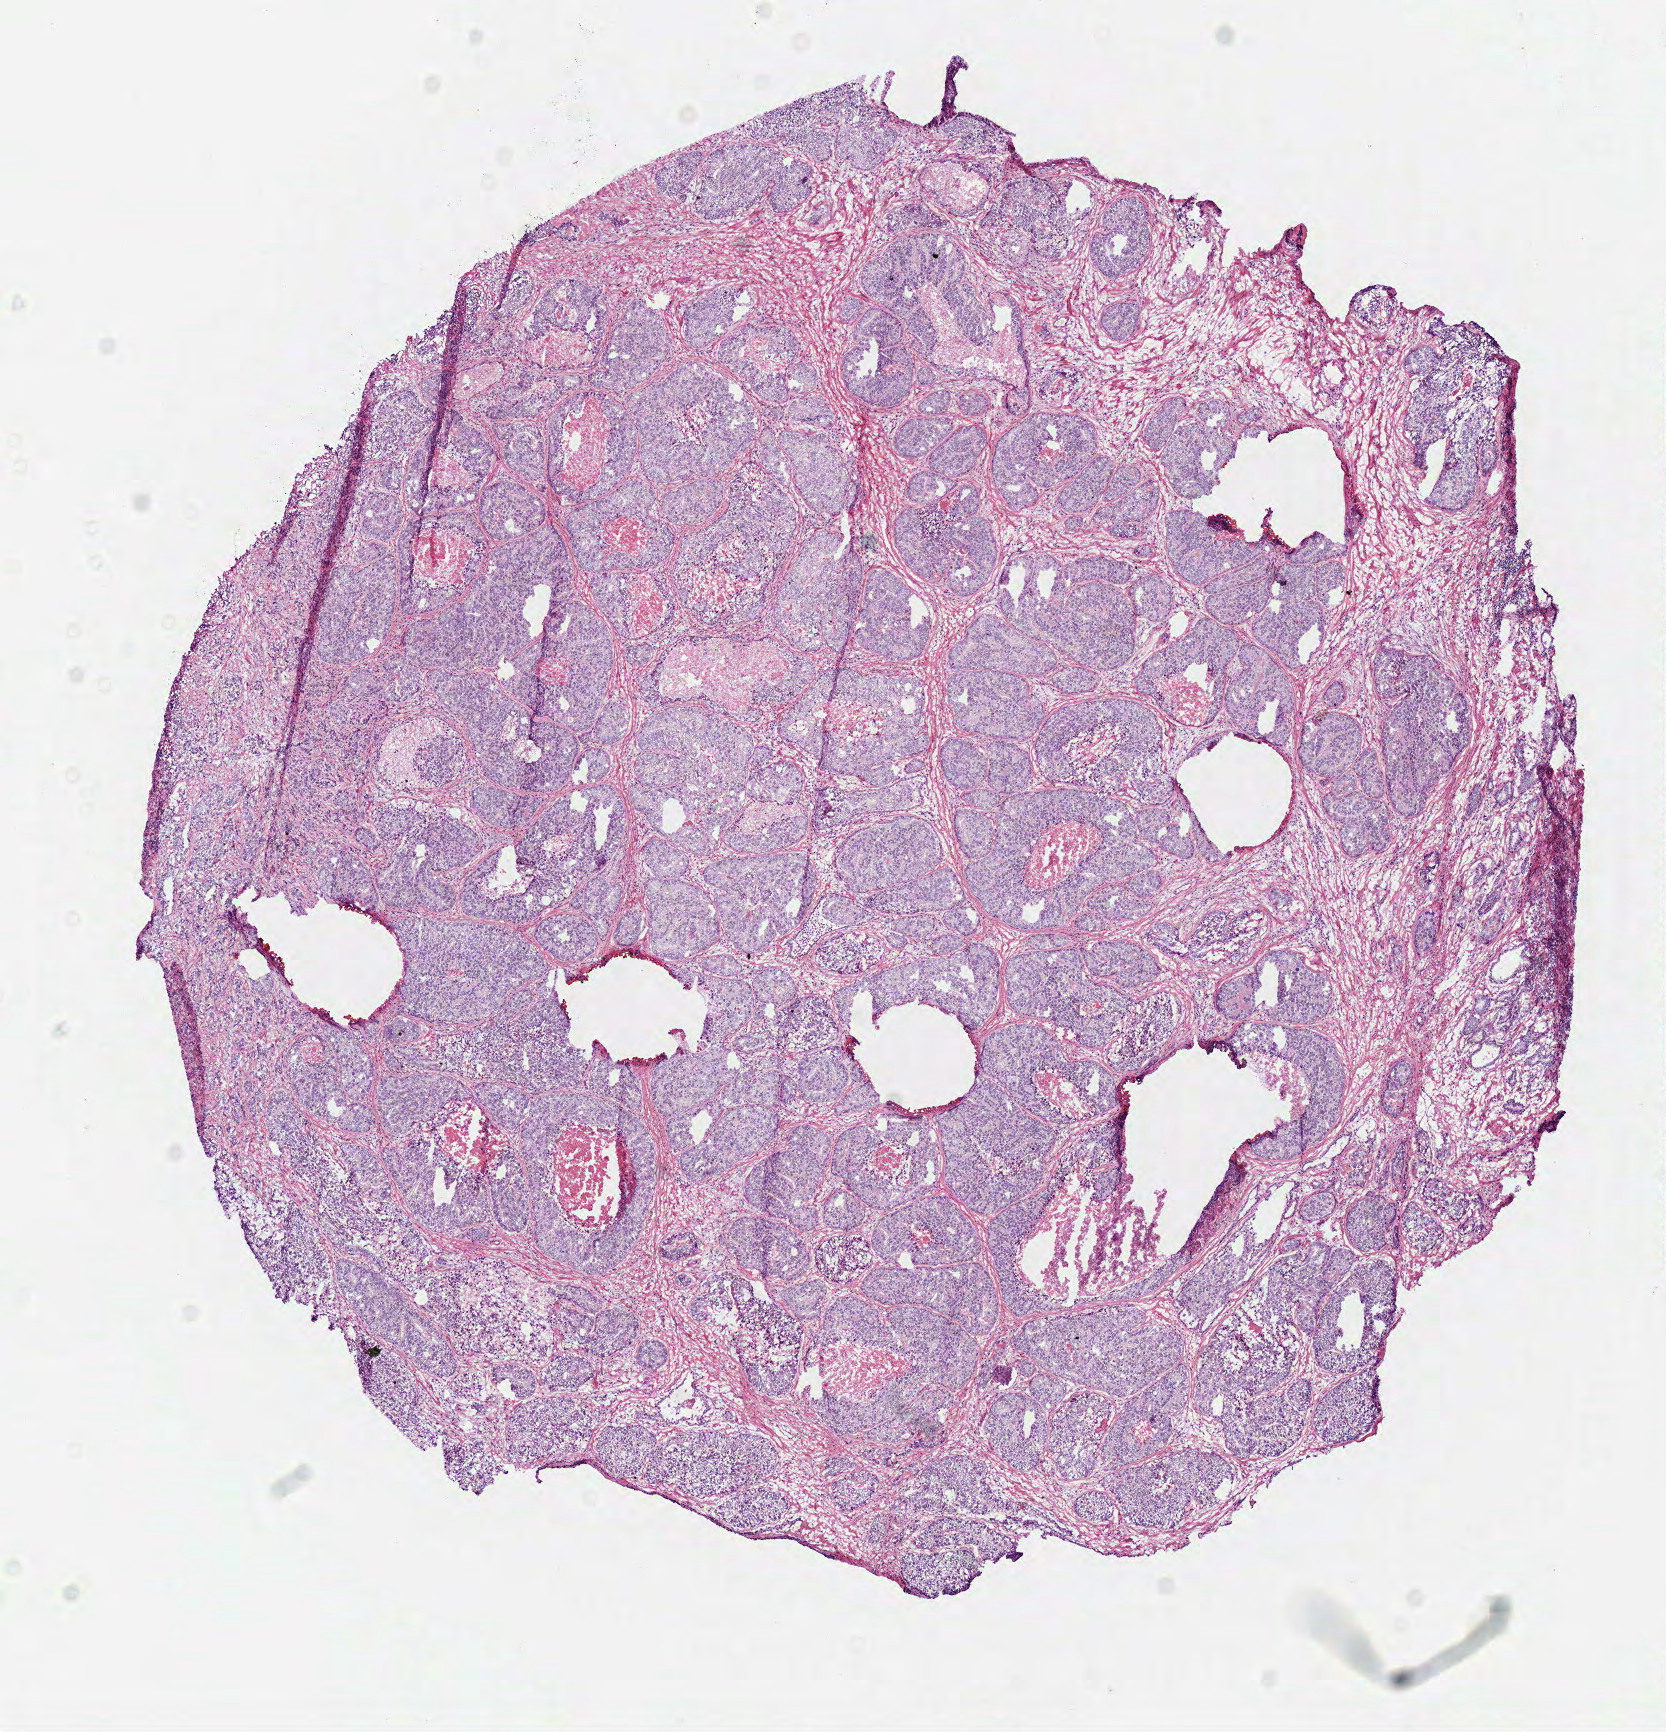
Digitized Hematoxylin and eosin (H&E) stained tissue section (whole slide) — shown as a low-resolution overview of the whole scanned area (about 6.6 x 6.8 mm); frozen section from the top of the tissue portion; prostate, primary tumour sample. Male patient; age at initial diagnosis 53 years. Gleason score: 9 (4+5). Composition of this section per pathologist review: tumour cells 90%, tumour nuclei 90%, normal cells 0%, stromal cells 8%, necrosis 2%.
Lymph nodes positive (case pathology): 0 of 4 examined. Diagnosis: Acinar cell carcinoma (prostate gland).